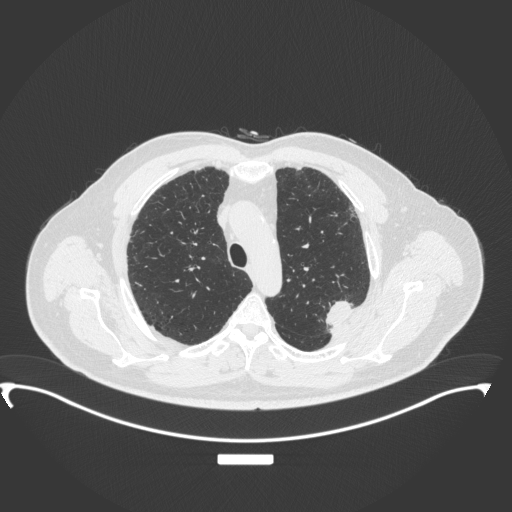
Chest CT, one axial slice; position 273 of 350 along the scan axis; lung window (W 1500 / L -600 HU); 512 × 512 image matrix, field of view 459 × 459 mm. Male patient, age 64 years. Case-level facts recorded for this patient, not image findings: clinical TNM (as recorded): T1c N1 M1.
Annotated regions visible in this slice (bounding box drawn by a radiologist):
- lung tumour (recorded histology: adenocarcinoma): bounding box [x1, y1, x2, y2] px = [321, 291, 358, 331]